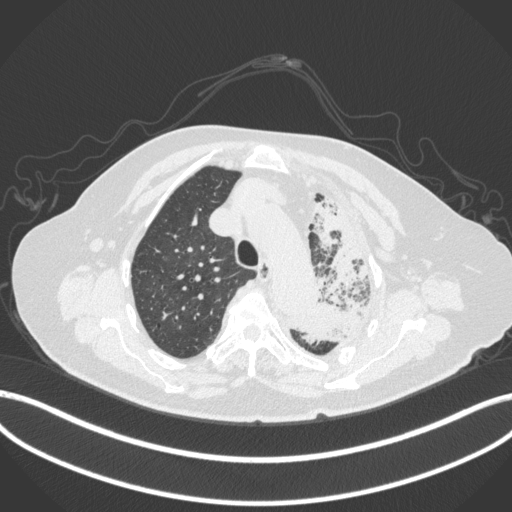
Chest CT, one axial slice; slice 299 of 399 in the series (ordered by position); reconstruction kernel B31f; 120 kVp; lung window (W 1500 / L -600 HU); 1 mm slice thickness; 512 × 512 image matrix, field of view 400 × 400 mm. Patient: female, 75 years. From the clinical record (not read from this slice): clinical TNM (as recorded): T3 N3 M1.
Annotated regions visible in this slice (bounding box drawn by a radiologist):
- lung tumour (recorded histology: adenocarcinoma): bounding box (x1, y1, x2, y2) in pixels: (287, 195, 382, 346)